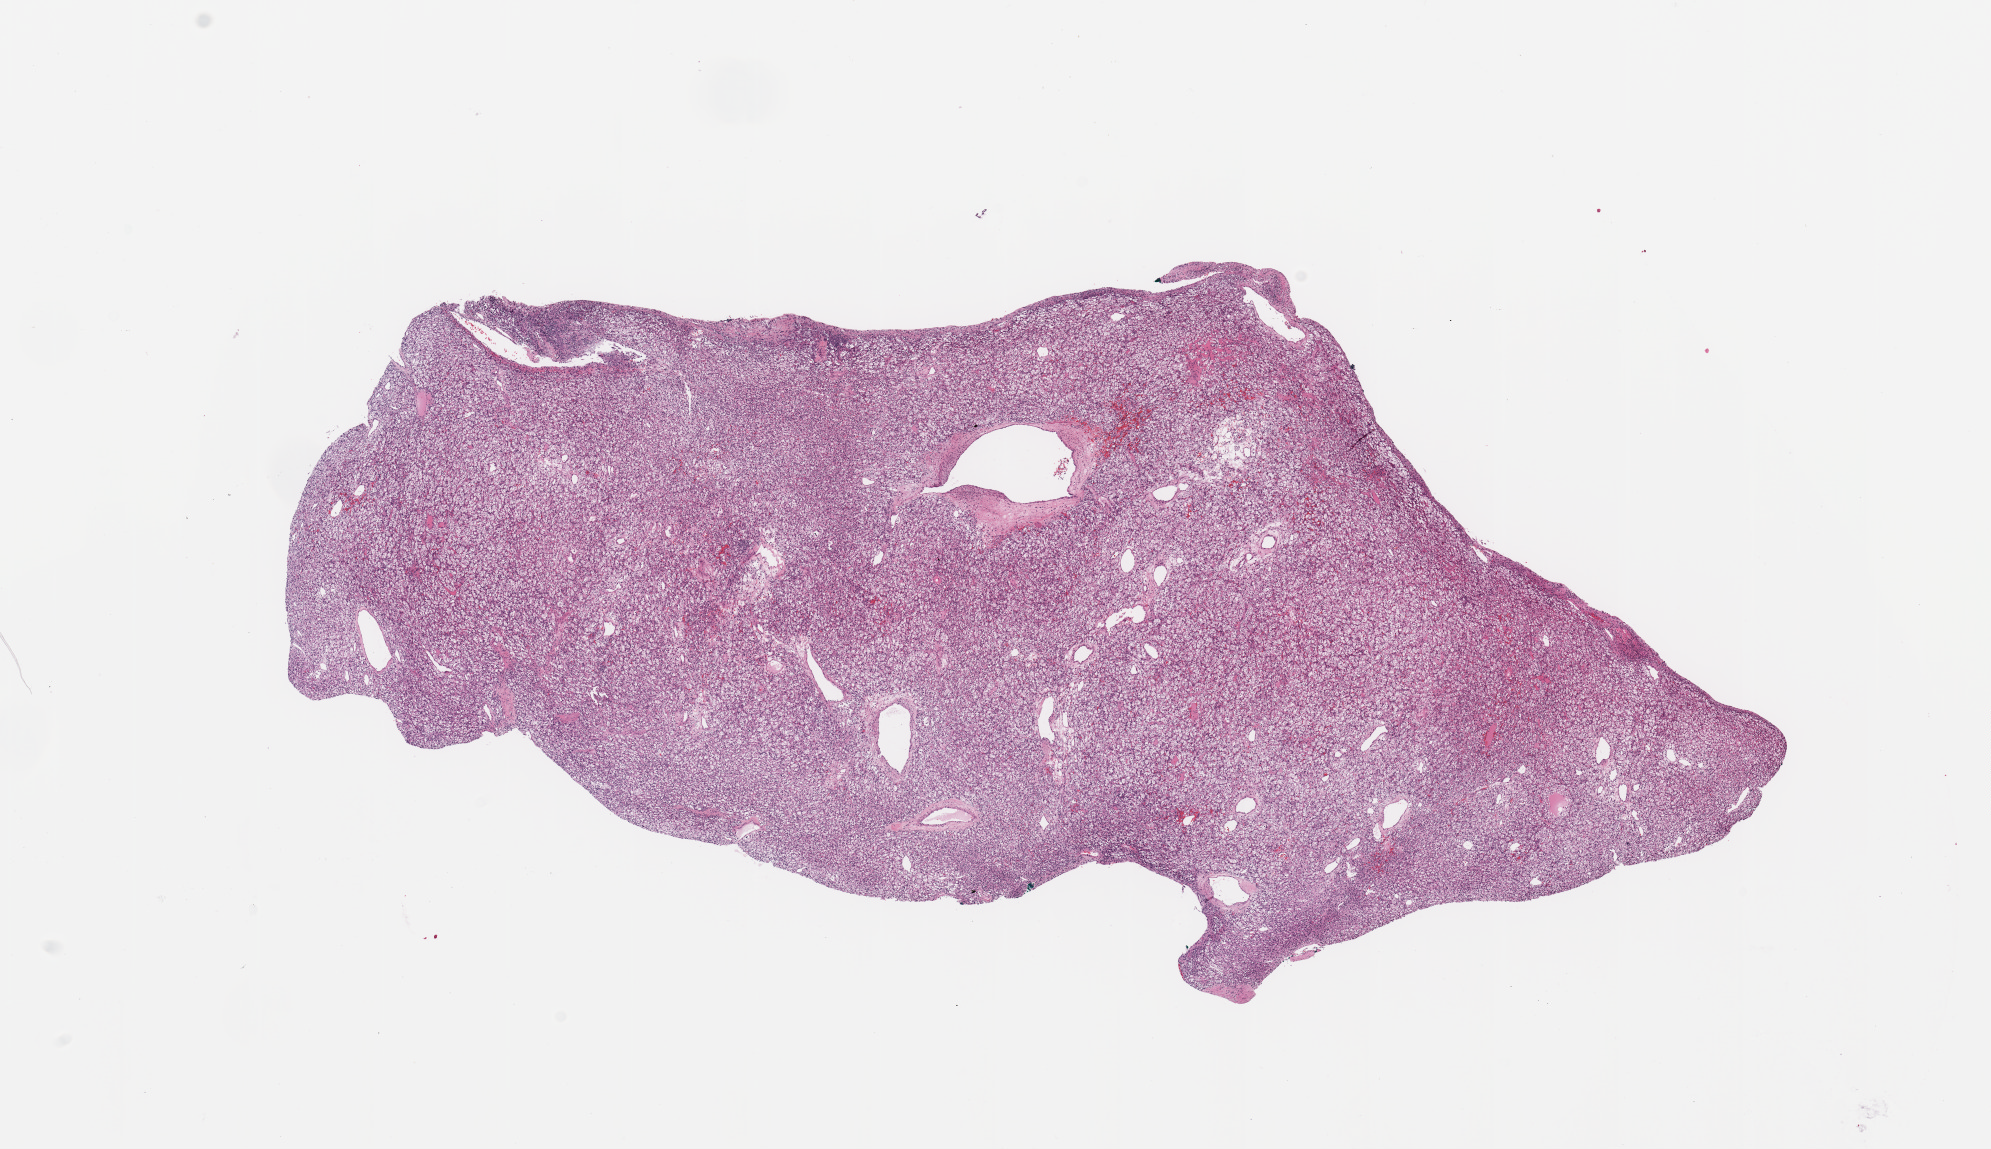
Digitized H&E tissue section (whole slide), low-resolution overview of the scanned area, about 15.8 x 9.1 mm (slide scanned at 20x); tumour tissue sample, sampled site: kidney. Female, 59 y/o. Histologic grade: G2 (moderately differentiated). Composition of this section per pathologist review: tumour nuclei 90%, necrosis 0%.
- primary tumour site (as recorded): lower pole
- diagnosis: Renal cell carcinoma, NOS
- AJCC pathologic stage: I